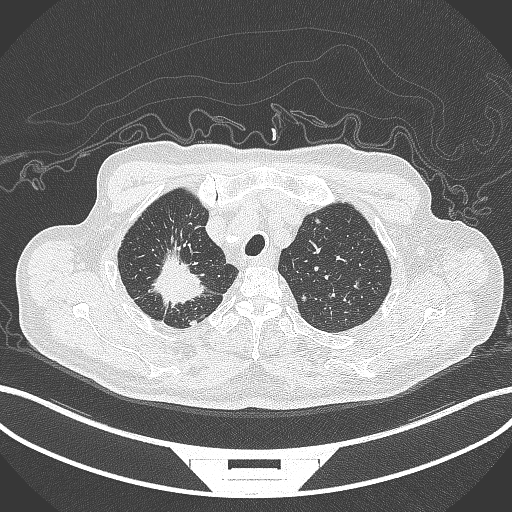
Chest CT, one axial slice; position 324 of 407 along the scan axis; reconstruction kernel B70f; lung window (W 1500 / L -600 HU); 1 mm slice thickness; 512 × 512 image matrix. Male patient, age 69 years. From the clinical record (not read from this slice): clinical TNM (as recorded): T1c N1 M1.
Annotated regions visible in this slice (bounding box drawn by a radiologist):
- lung tumour (recorded histology: adenocarcinoma): box from (x=142, y=246) to (x=205, y=311) px